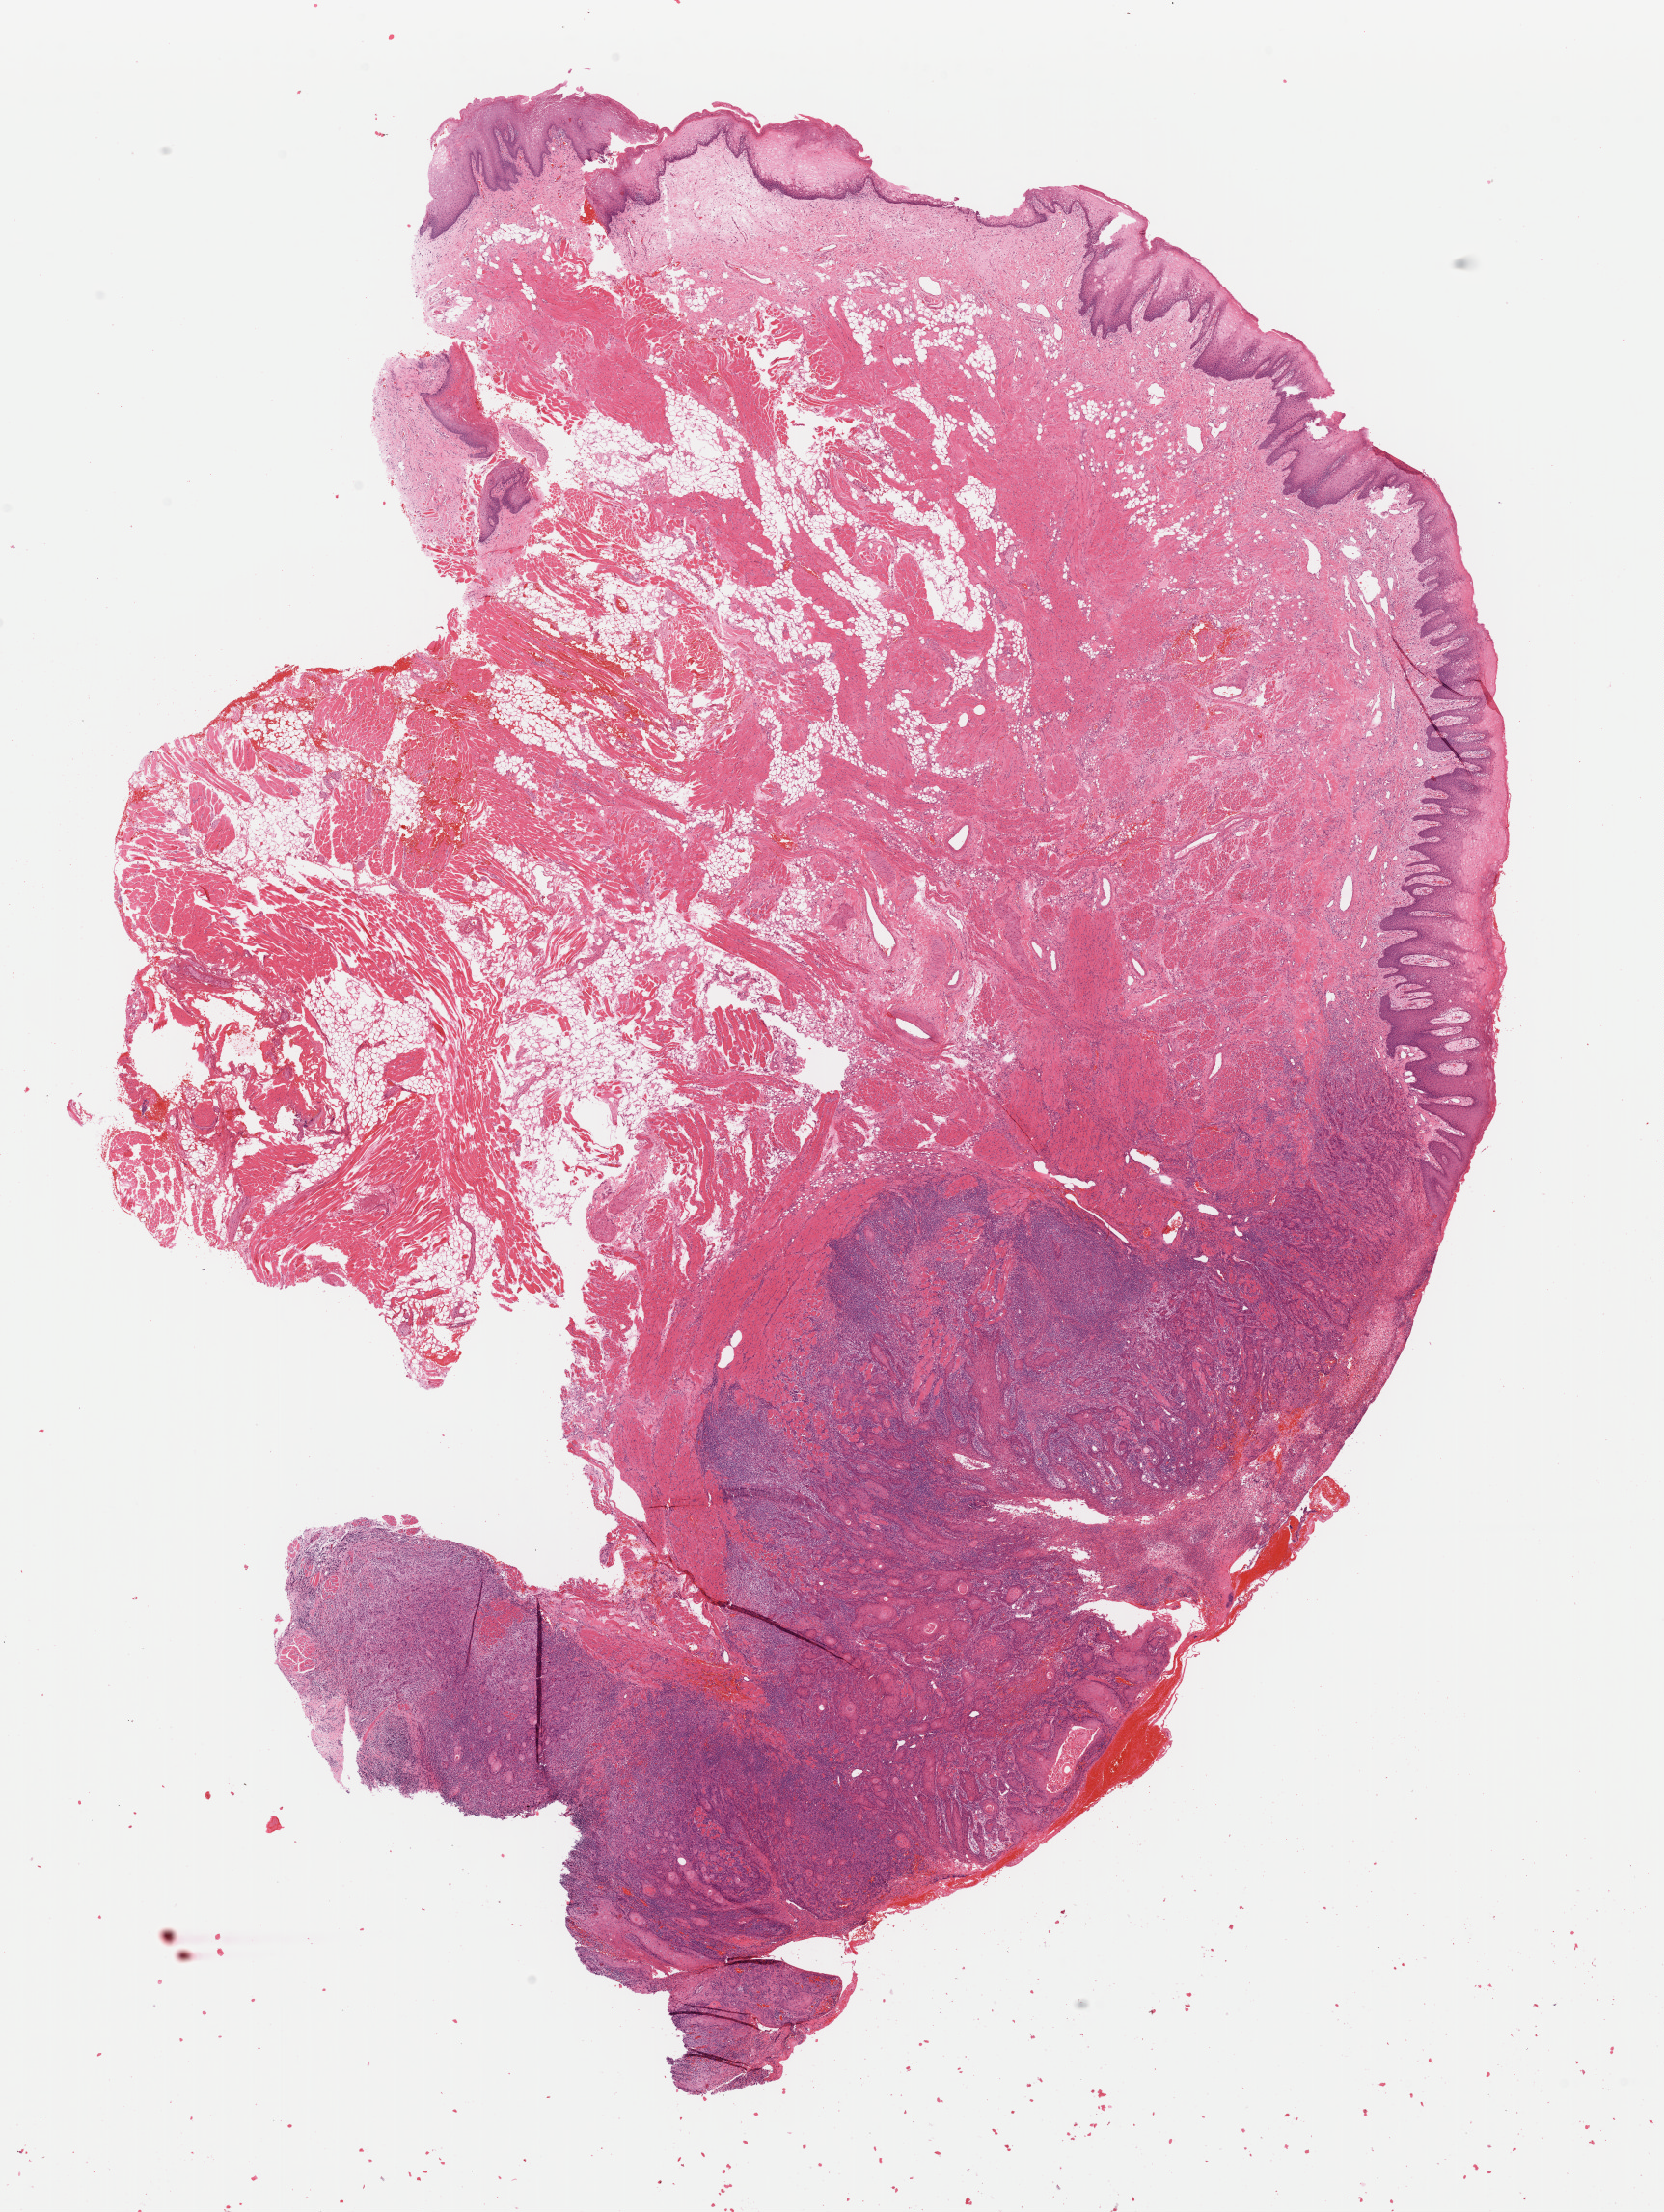
Digitized H&E-stained tissue section (whole slide), a low-resolution overview of the entire scanned area, about 13.6 x 18.1 mm (slide scanned at 40x), FFPE section, sample: primary tumour, head and neck. Patient: male, age at initial diagnosis 47 years. Histologic grade: G1 (well differentiated).
- histologic diagnosis: Squamous cell carcinoma, keratinizing, NOS
- AJCC pathologic stage: III (7th edition)